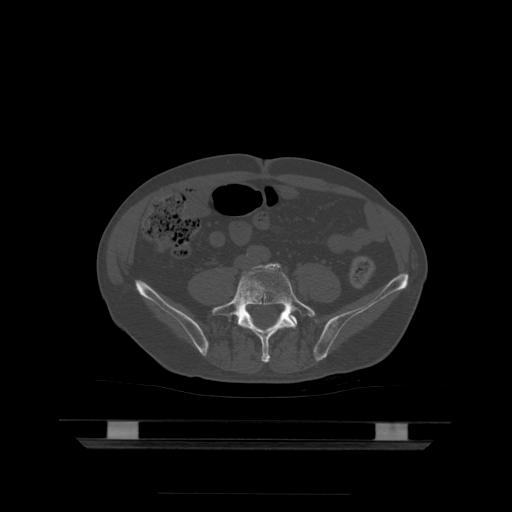
CT including the spine, one axial slice. Position 74 of 522 along the scan axis. Bone window (W 1800 / L 400 HU). 1.25 mm slice thickness. 512 × 512 image matrix, field of view 436 × 436 mm. Patient age 68 years. Case-level facts recorded for this patient, not image findings: primary cancer: urothelial.
Structures marked on this image (semi-automatic segmentation, software-assisted and operator-edited):
- L5 vertebra: bounding box (x1, y1, x2, y2) in pixels: (212, 263, 316, 363)